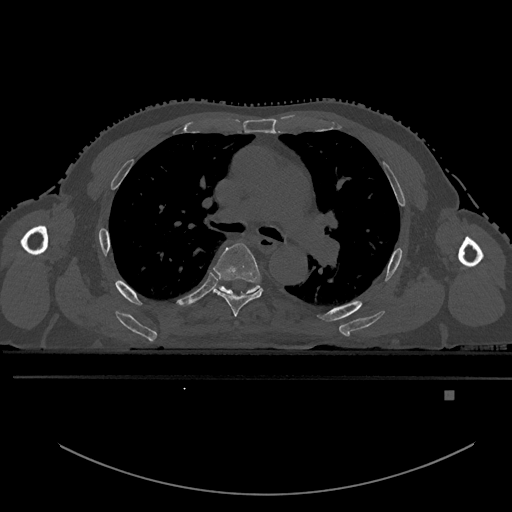
CT including the spine, one axial slice. Slice 347 of 969 in the series (ordered by position). Bone window (W 1800 / L 400 HU). 512 × 512 image matrix, field of view 456 × 456 mm. Patient: male, 82 years. From the clinical record (not read from this slice): primary cancer: prostate; vertebrae with lytic lesions (as recorded): T11, T9, T8, T2.
Structures marked on this image (semi-automatically segmented with operator editing):
- T5 vertebra: box from (x=213, y=242) to (x=263, y=317) px
- T6 vertebra: (x=215, y=284)–(x=261, y=297)